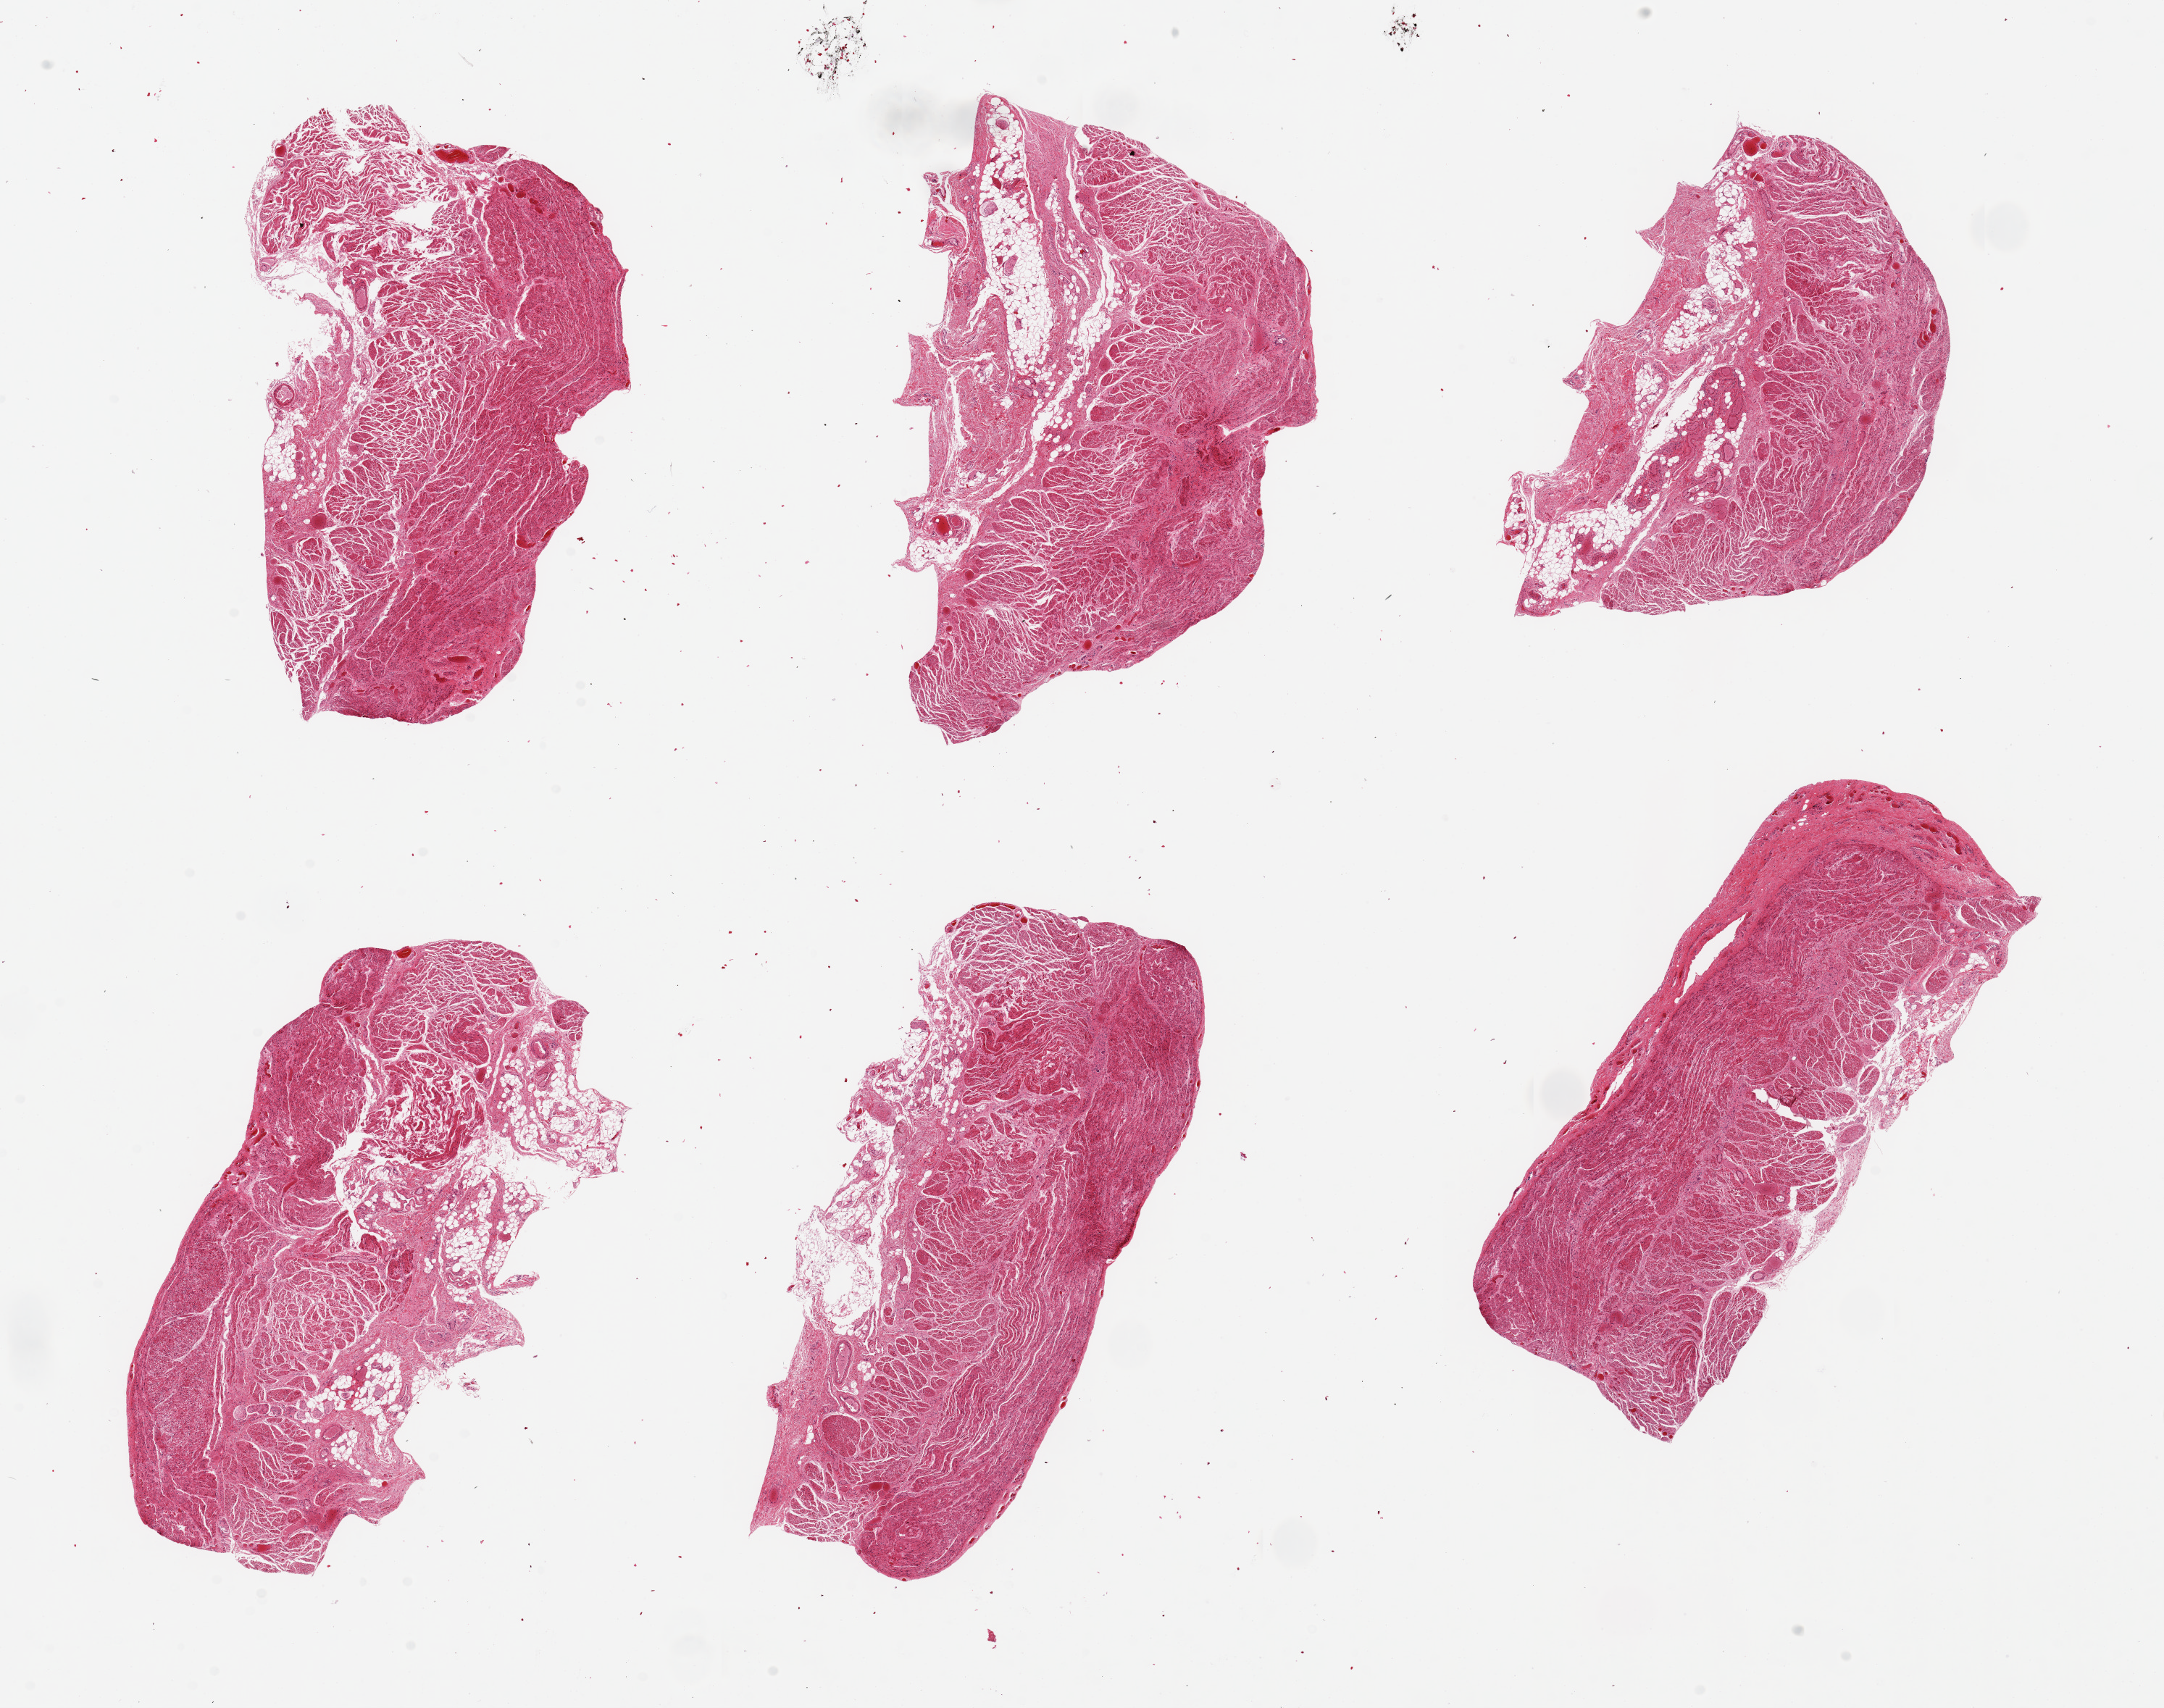
Hematoxylin and eosin (H&E) whole-slide image, brightfield — low-resolution overview of the scanned area, about 23.6 x 18.7 mm (from a 20x scan). PAXgene-fixed, paraffin-embedded tissue. Target tissue: gastroesophageal junction. Donor tissue sample. Female donor.
Pathologist's review note for this sample: 6 pieces ~7x3mm; all muscularis; good specimens.